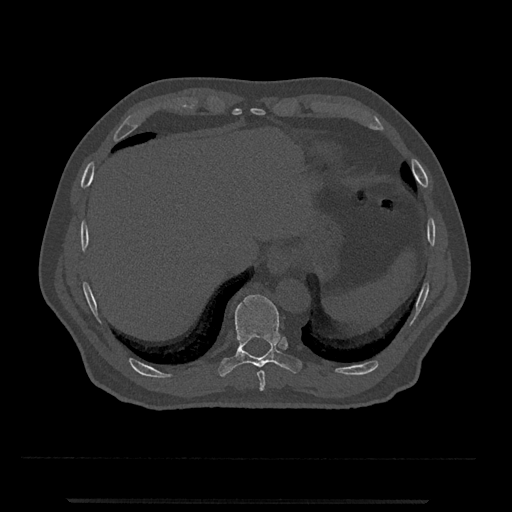
CT including the spine, one axial slice; slice 527 of 797 in the series (ordered by position); 120 kVp; bone window (W 1800 / L 400 HU); 0.5 mm slice thickness; 512 × 512 image matrix, field of view 419 × 419 mm. Patient: male, 63 years. Case-level facts recorded for this patient, not image findings: primary cancer: prostate.
Structures marked on this image (semi-automatic segmentation, software-assisted and operator-edited):
- T10 vertebra: bounding box [x1, y1, x2, y2] px = [218, 295, 302, 377]
- T9 vertebra: [257, 371, 265, 391]